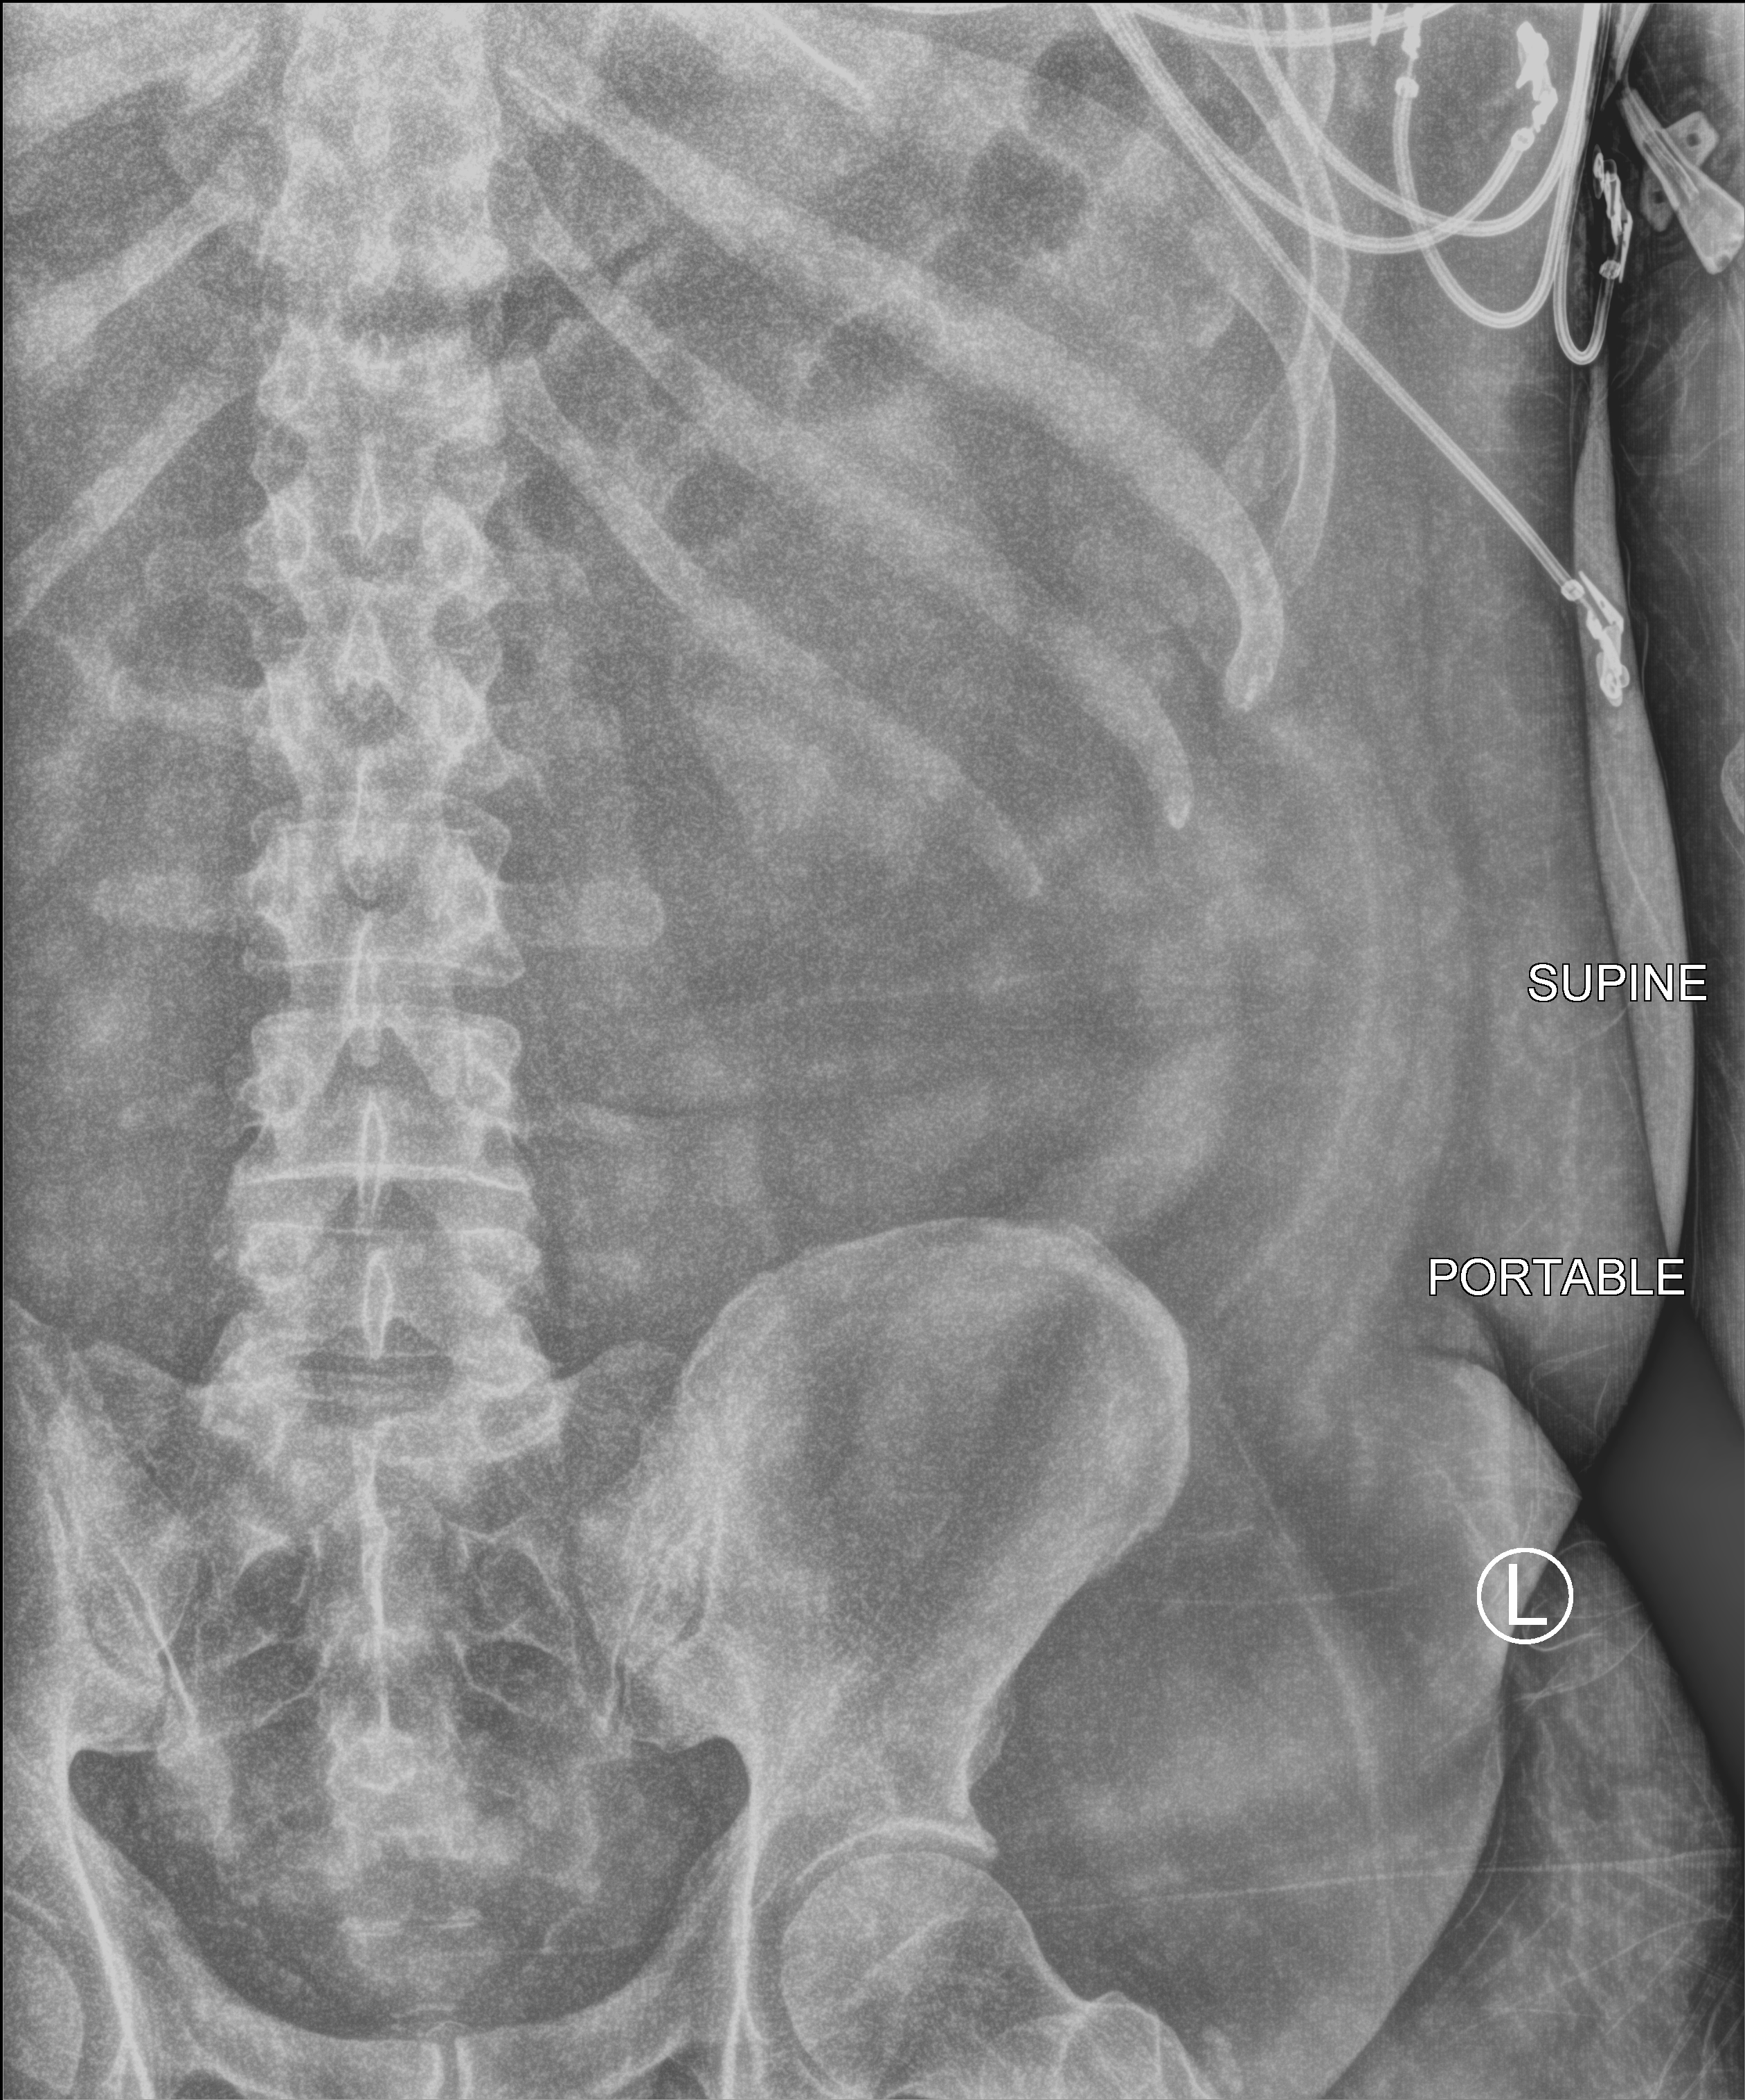
Bedside abdomen radiograph (computed radiography), anteroposterior (AP) projection. Male patient hospitalised with COVID-19, age 18–59 years.
From the hospital-stay record, not from the radiograph (when in the stay this image was taken is not recorded): diabetes (admission record): no.